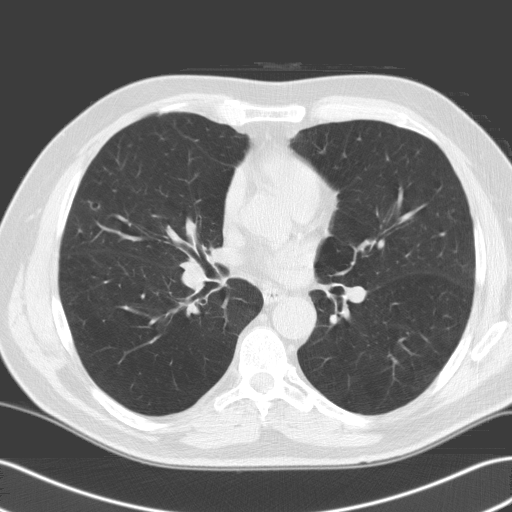
Chest CT (low-dose screening protocol), one axial image; baseline screening round; lung window (W 1500 / L -600 HU); standard (soft-tissue) reconstruction kernel (C); slice 76 of 160 in the series; 512 × 512 image matrix, field of view 357 × 357 mm. Male participant, aged 65 years at enrolment. Former smoker at enrolment.
Expert reader's lesion annotation, bounding box (x1, y1, x2, y2) in pixels: (71, 189, 115, 228). No non-calcified nodule or mass ≥4 mm was recorded by the screening reader at this exam. Lung cancer was diagnosed 728 days after this screen: adenocarcinoma, NOS, right middle lobe, moderately differentiated (G2), stage IA (AJCC 6th edition), 25 mm at pathology.